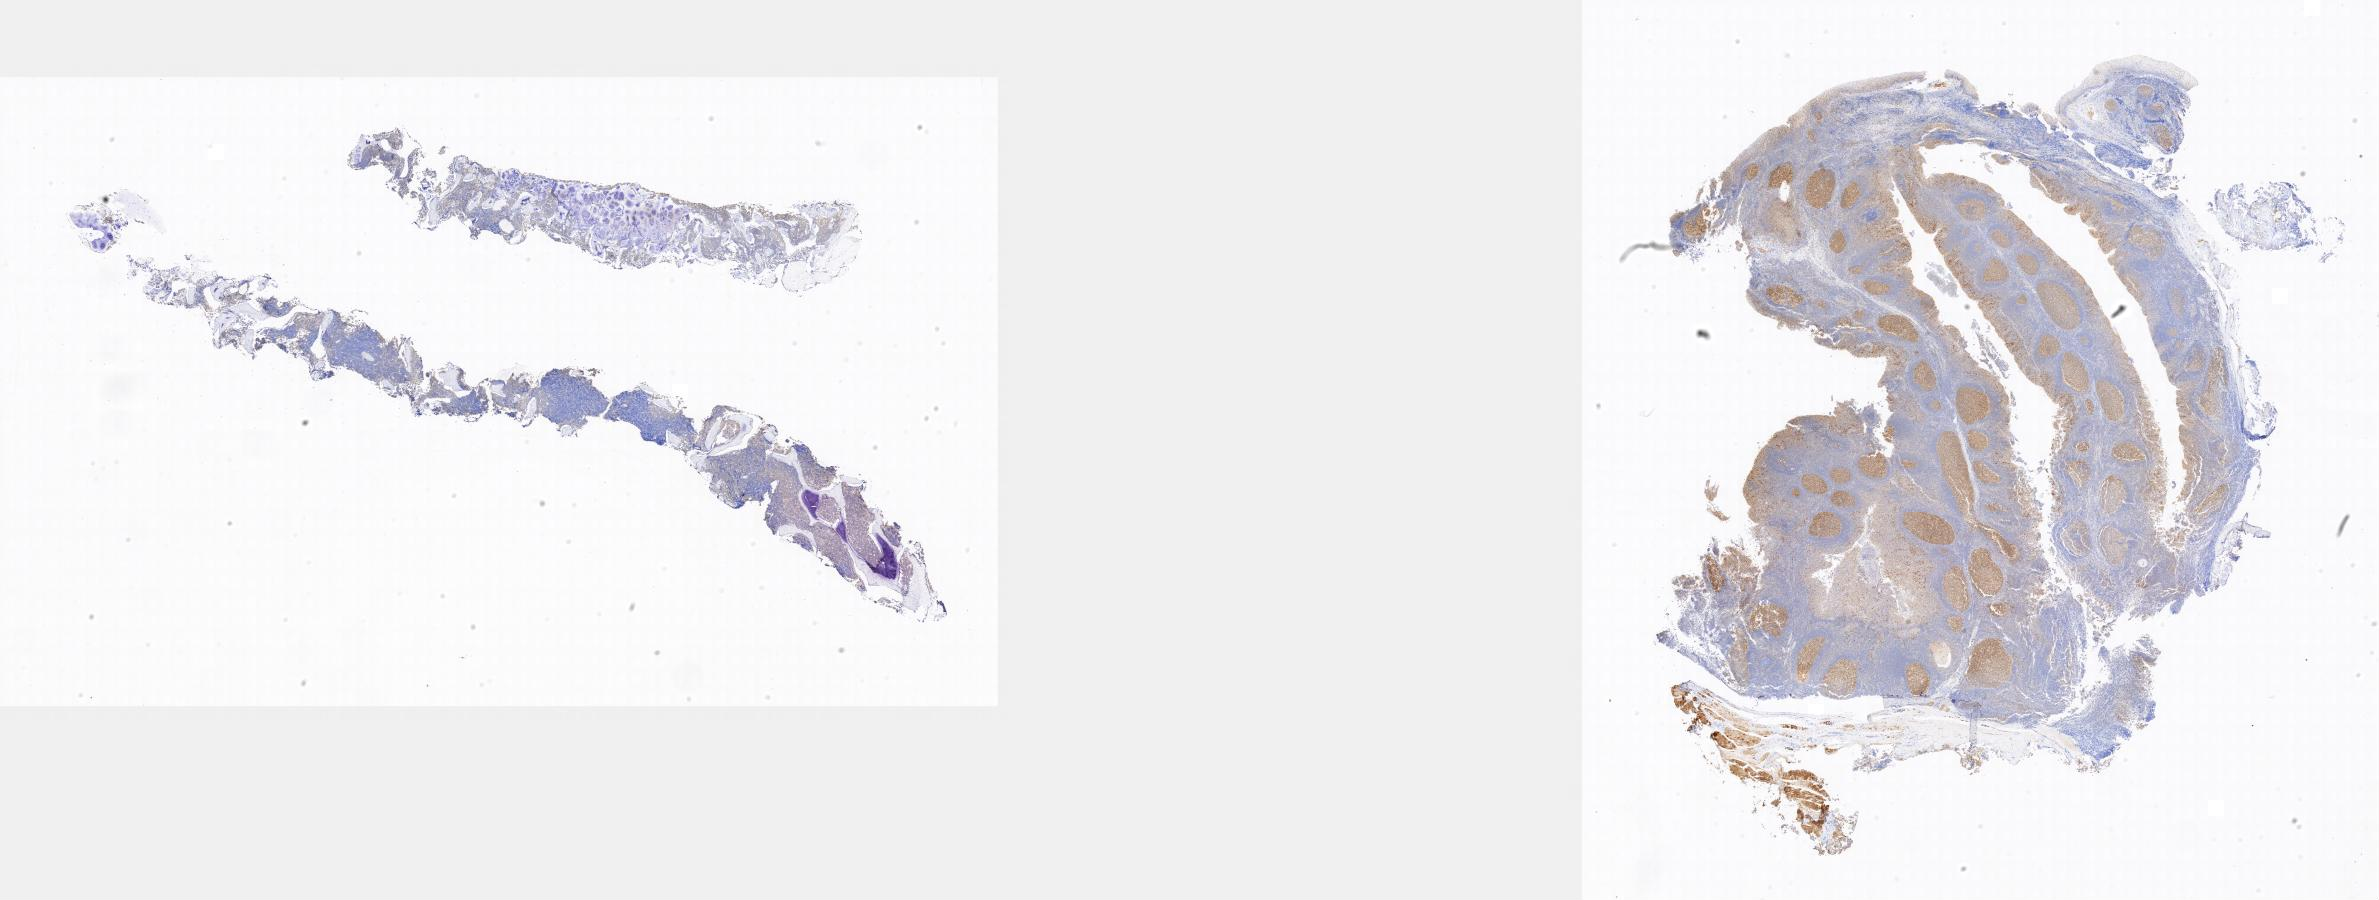
Whole-slide image, immunohistochemical stain for BCL6 — a low-resolution overview of the entire scanned area, tumor tissue, site: bone marrow. Male patient, age 11 years.
Diagnosis: Burkitt lymphoma, NOS.